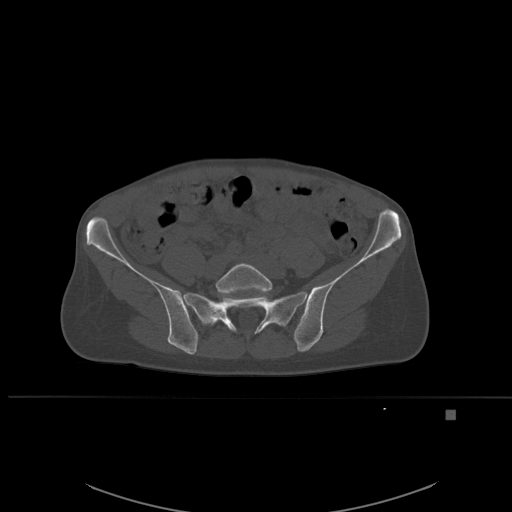
CT including the spine, one axial slice; slice 163 of 537 in the series (ordered by position); bone window (W 1800 / L 400 HU); 1.5 mm slice thickness; 512 × 512 image matrix, field of view 440 × 440 mm. Patient: female, 45 years. Case-level facts recorded for this patient, not image findings: primary cancer: lung.
Structures marked on this image (semi-automatically segmented with operator editing):
- L5 vertebra: bounding box <216,262,272,297> (left, top, right, bottom; pixels)